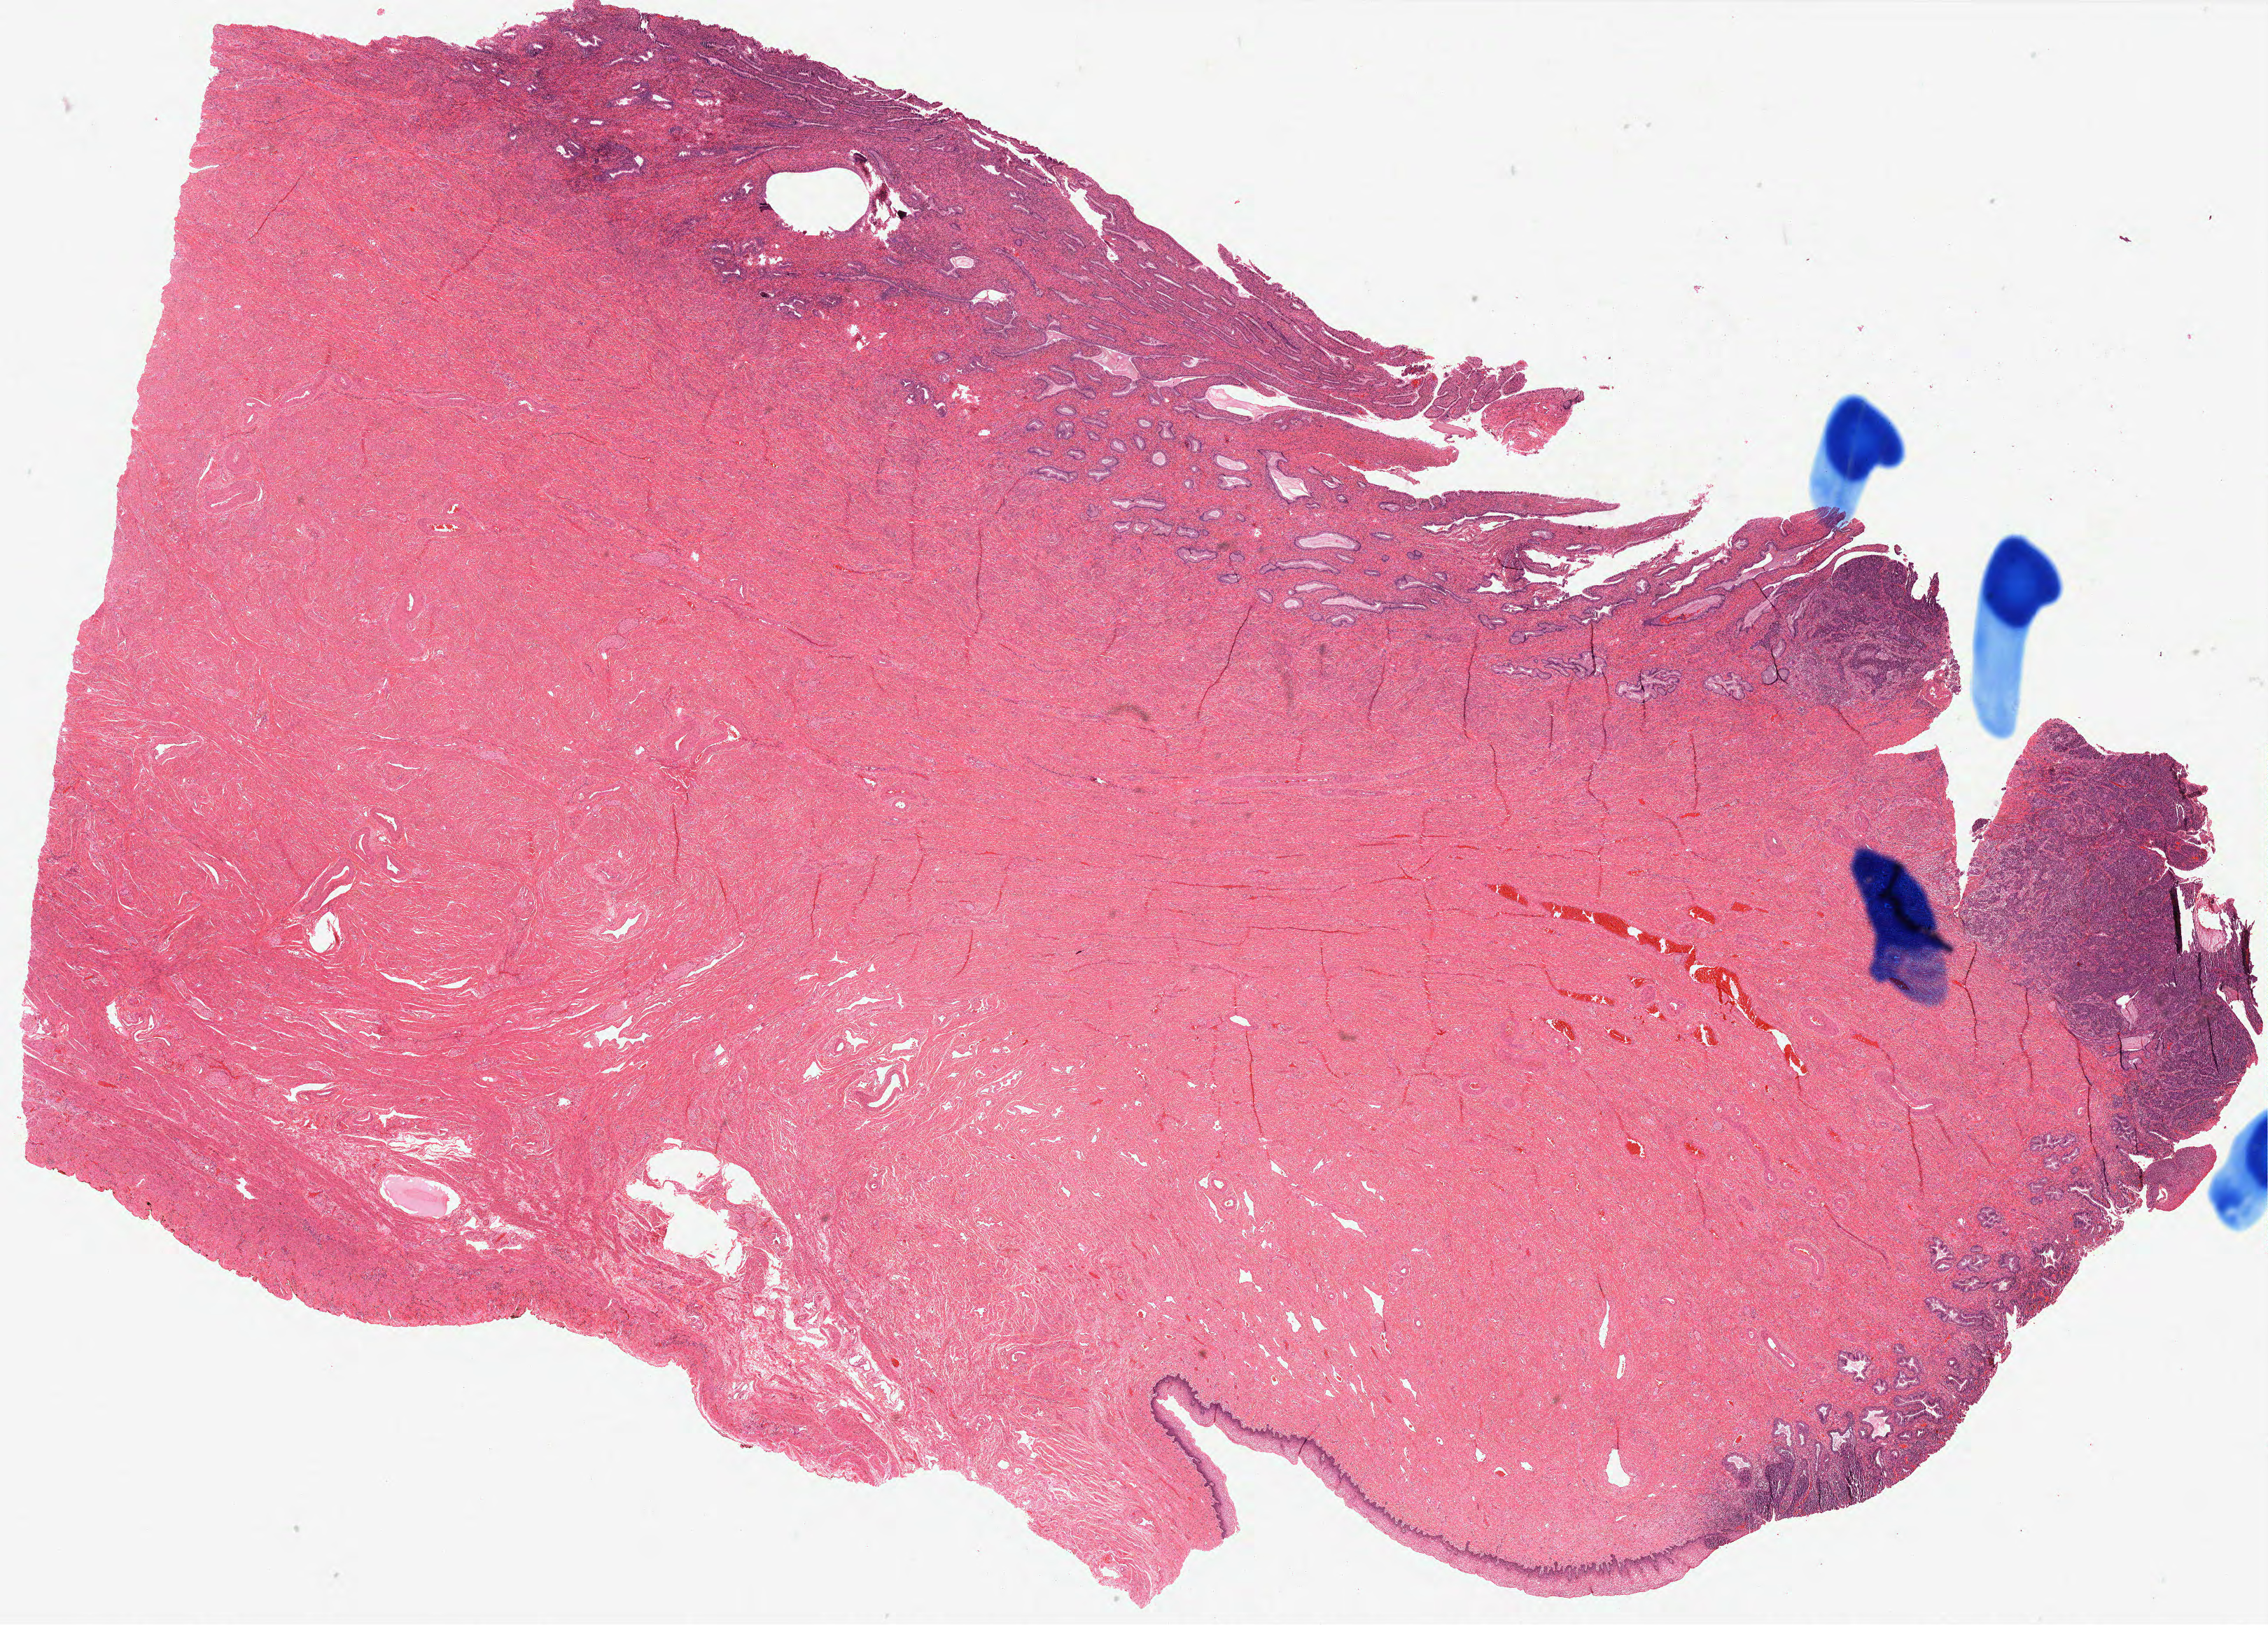
Whole-slide histology image, H&E-stained — whole scanned area (about 25.9 x 18.6 mm, from a 40x scan) shown as a low-resolution overview. FFPE section. Cervix, primary tumour sample. Patient: female, age at initial diagnosis 26 years. Histologic grade: G2 (moderately differentiated).
* FIGO stage: IB1
* pathologic diagnosis: Squamous cell carcinoma, NOS